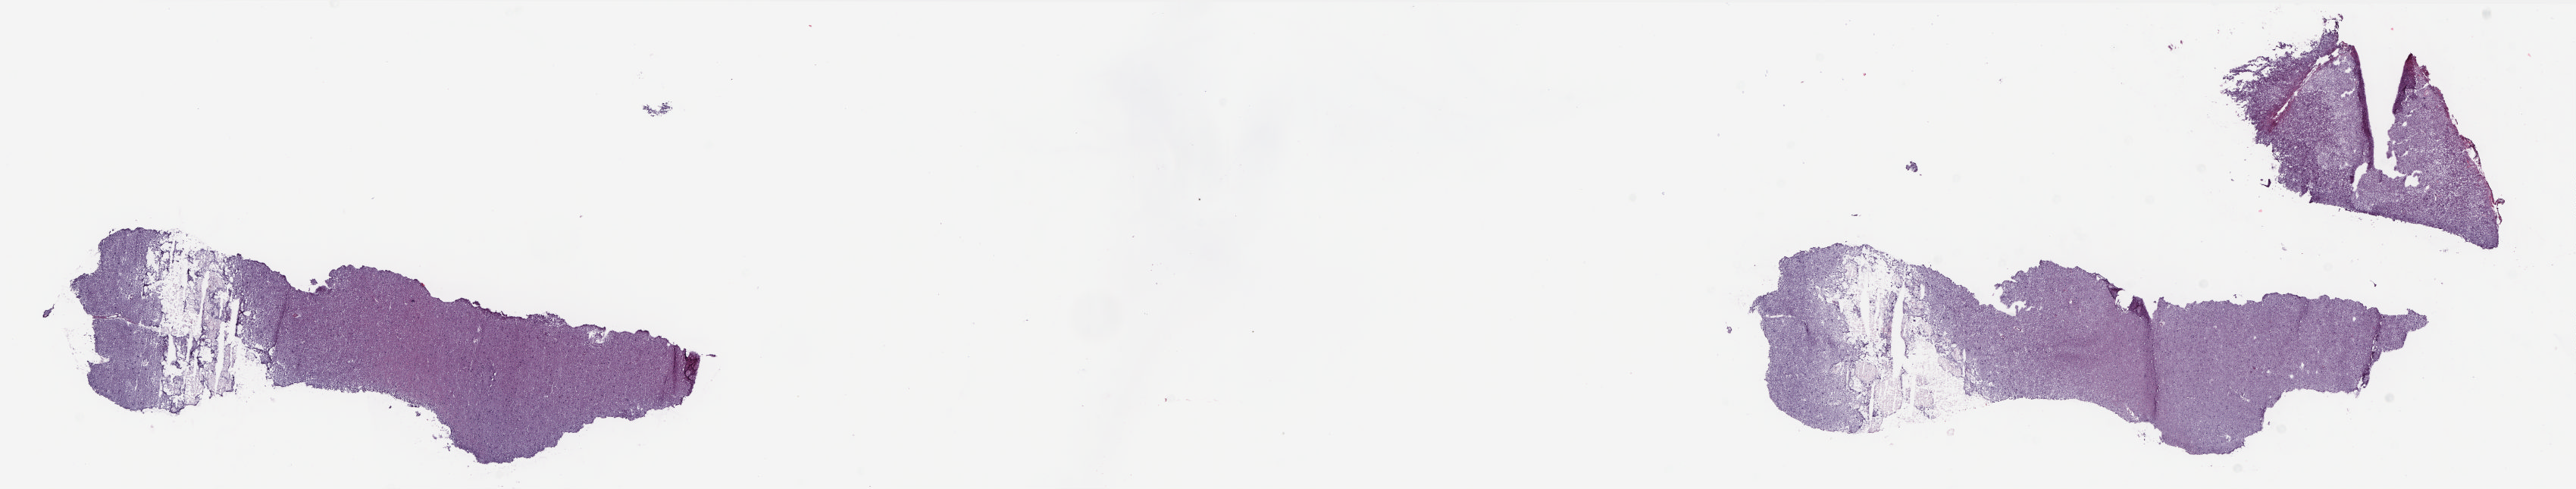
Digitized H&E tissue section (whole slide), shown as a low-resolution overview of the whole scanned area (about 27.4 x 5.2 mm, acquisition: 20x scan); frozen section; solid tissue normal (non-tumour tissue) sample from the brain. Pathologist review of this section (percent, as recorded): tumour cells 0%, tumour nuclei 0%, normal cells 25%, stromal cells 75%, necrosis 0%. Inflammatory infiltration, as recorded: lymphocyte infiltration 0%, monocyte infiltration 0%, neutrophil infiltration 0%.
* this section: solid tissue normal sample (biorepository sample class)